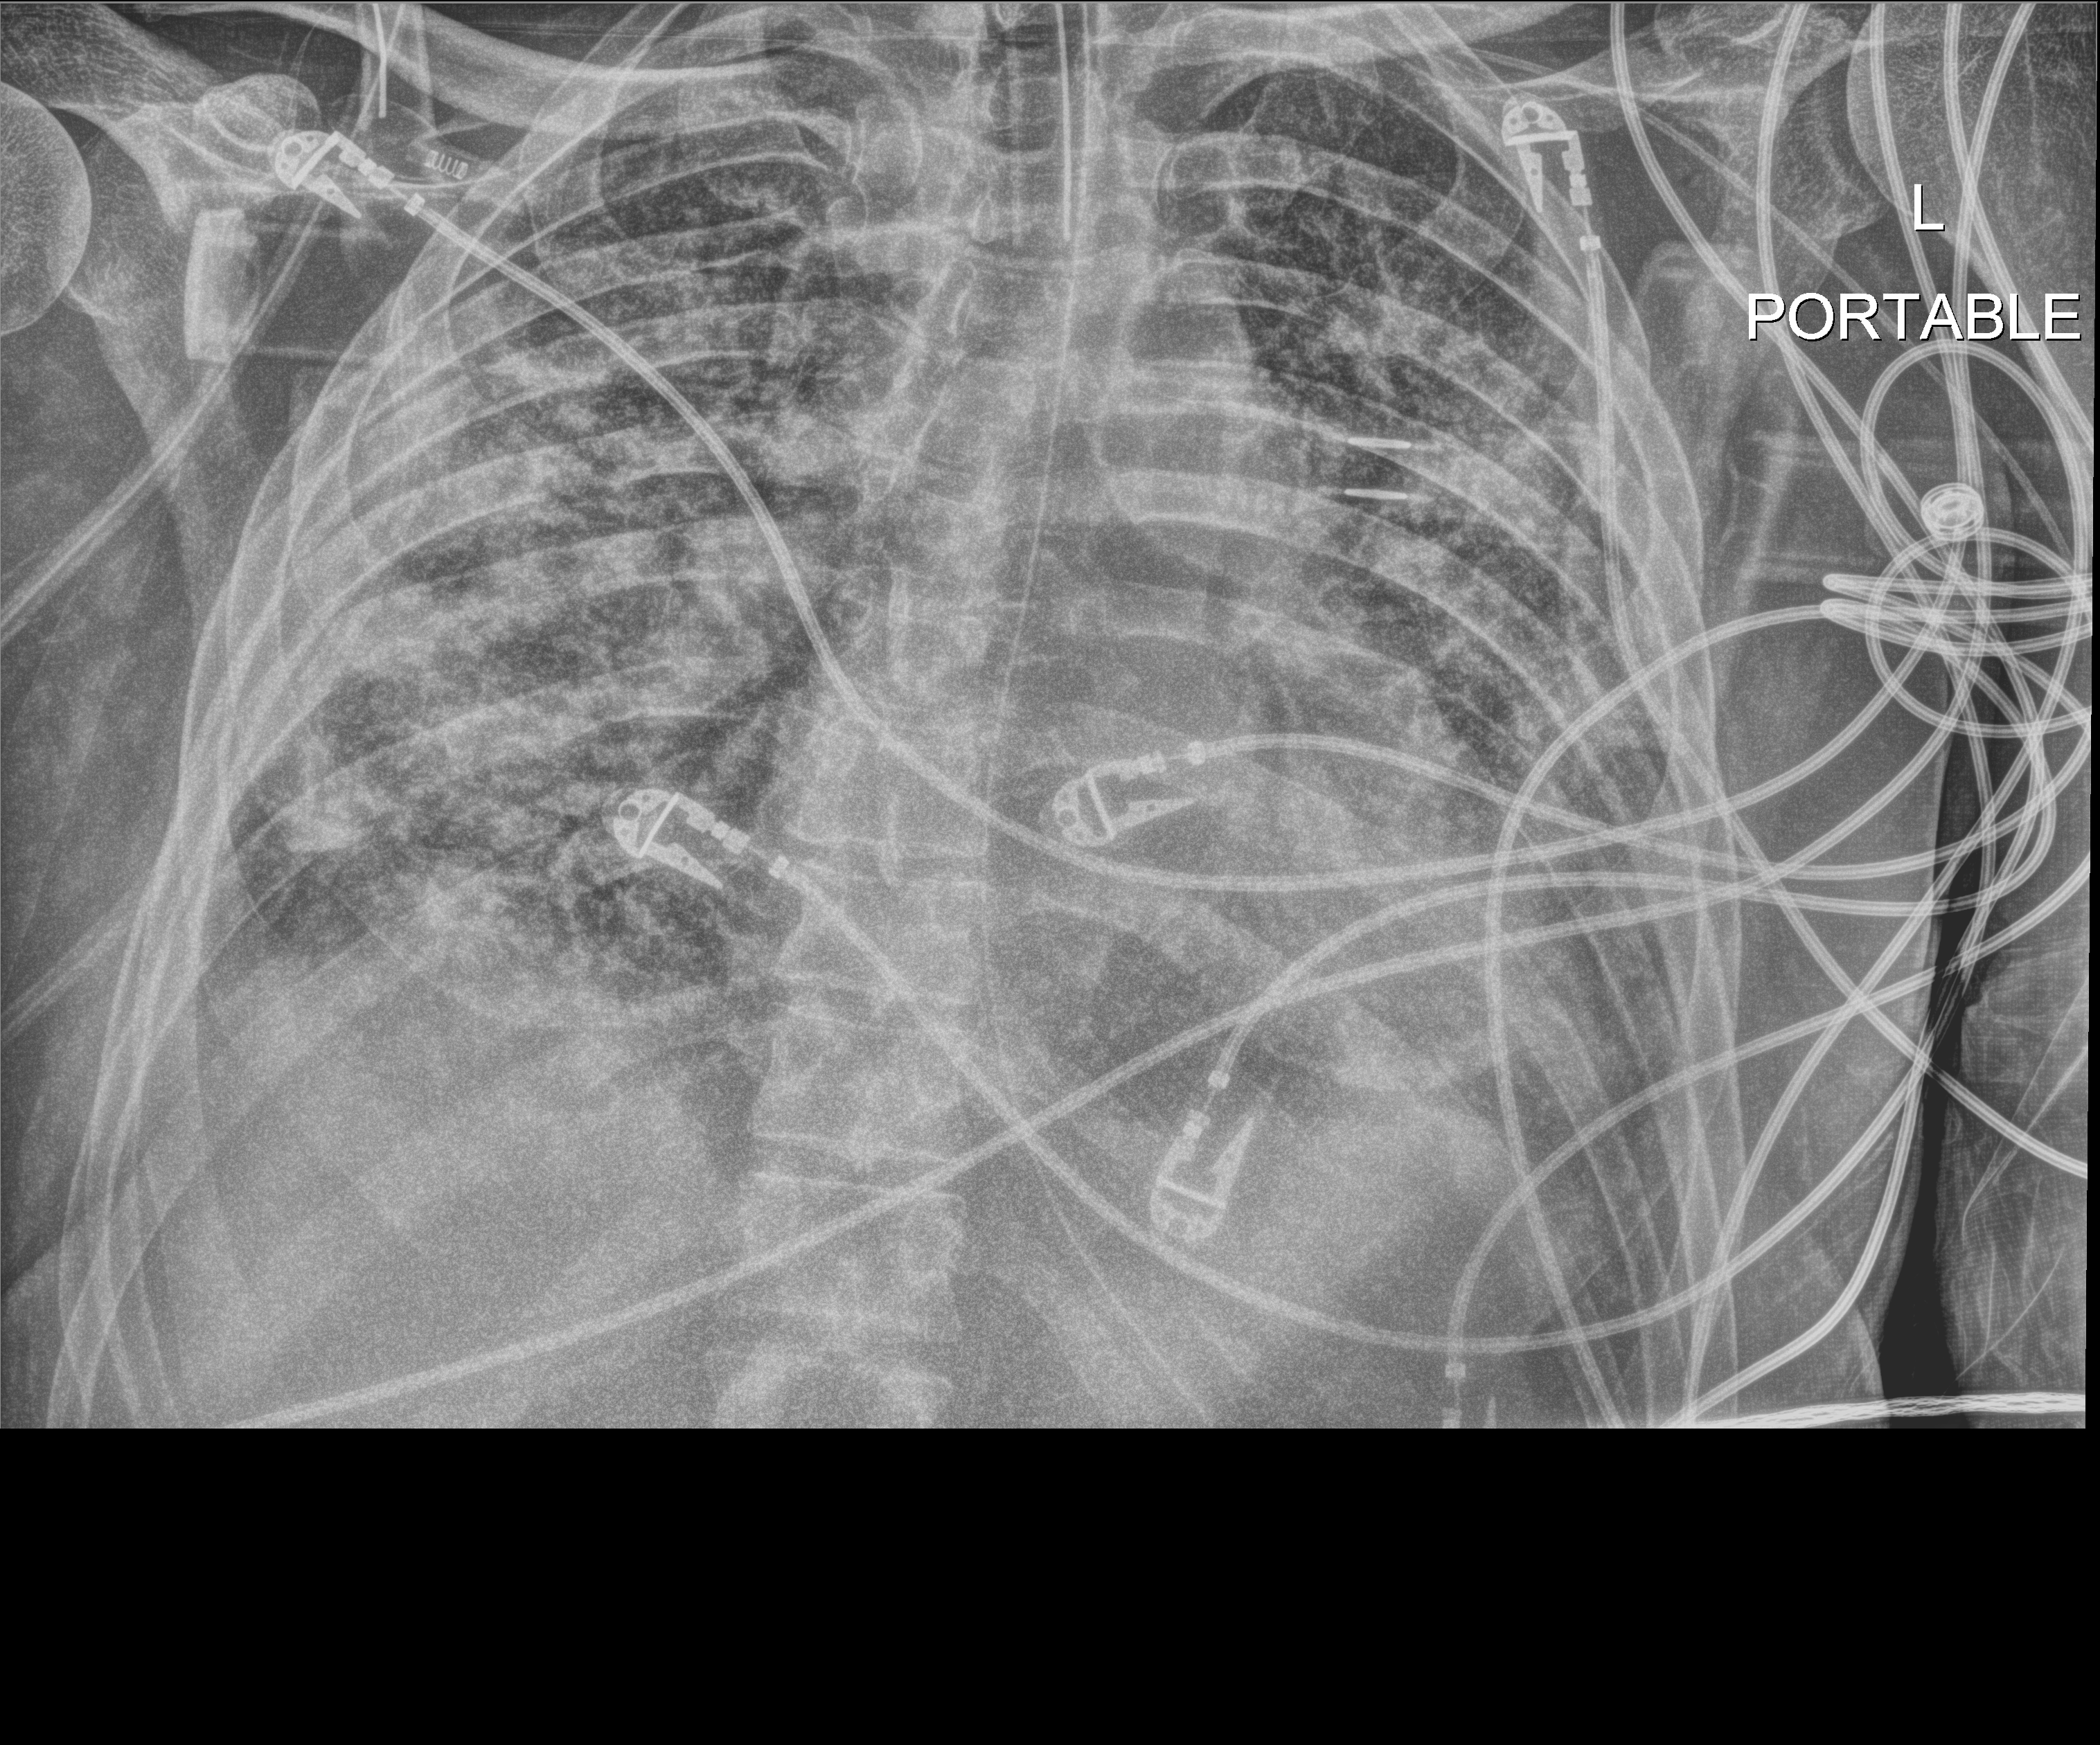
Bedside chest radiograph (digital radiography), anteroposterior (AP) projection. Patient hospitalised with COVID-19; male, aged 18–59 years.
From the hospital-stay record, not from the radiograph (when in the stay this image was taken is not recorded):
- admitted to intensive care during this hospital stay: yes
- mechanically ventilated during this hospital stay: yes